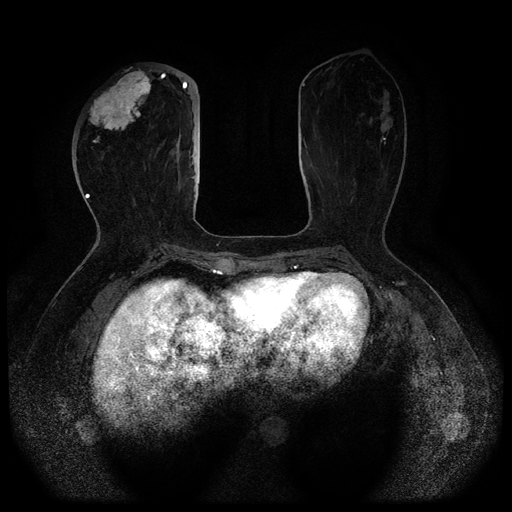
Breast MRI (dynamic contrast-enhanced, multi-phase), one axial slice. Slice 35 of 116 in the series (ordered by position). Dynamic contrast-enhanced series, time point 2 of 5 at this slice position (early post-contrast). 1.5 T. TE 2.6 ms, TR 5.3 ms. 512 × 512 image matrix, field of view 350 × 350 mm. Female patient, age 51 years.
Outlined on this slice (semi-automatic segmentation, software-assisted and operator-edited):
- breast lesion (labelled 'tumour' in the annotation; benign lesions carry a separate 'benign' label): bounding box (x1, y1, x2, y2) in pixels: (88, 67, 151, 143)